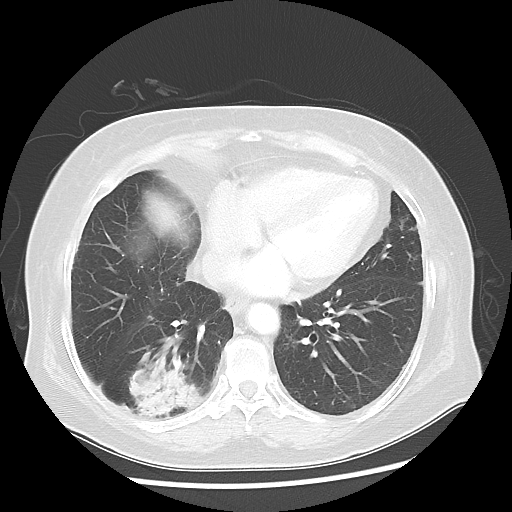
Chest CT, one axial slice; reconstruction kernel LUNG; 120 kVp; lung window (W 1500 / L -600 HU); 5 mm slice thickness; 512 × 512 image matrix, field of view 360 × 360 mm. Patient: female, 64 years. From the clinical record (not read from this slice): clinical TNM (as recorded): Tis N0 M0.
Annotated regions visible in this slice (bounding box drawn by a radiologist):
- lung tumour (recorded histology: adenocarcinoma): bounding box <117,348,208,435> (left, top, right, bottom; pixels)